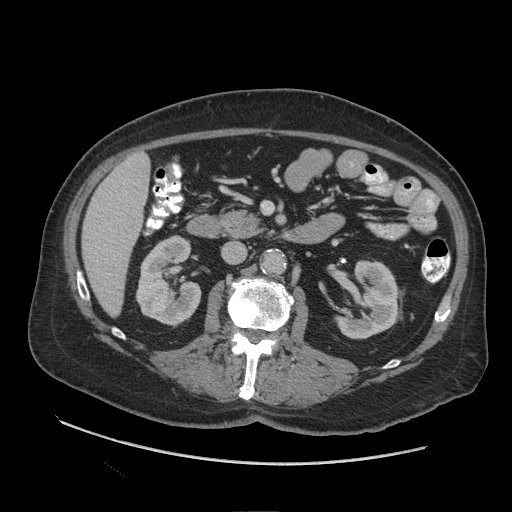
Contrast-enhanced abdominal CT (liver protocol), one axial slice; position 35 of 109 along the scan axis; 140 kVp; soft-tissue window (W 400 / L 40 HU); 512 × 512 image matrix, field of view 420 × 420 mm. From the clinical record (not read from this slice): diagnosis: hepatocellular carcinoma (patient treated with transarterial chemoembolisation; whether this scan precedes or follows treatment is not stated here); TNM stage (as recorded): Stage-I; Child-Pugh class: A; tumour nodularity: uninodular.
Outlined on this slice (semi-automatically segmented with operator editing):
- liver parenchyma outside the tumour (the mass and vessels are separate outlines, so this box may not span the whole liver): bounding box [x1, y1, x2, y2] px = [82, 152, 150, 316]